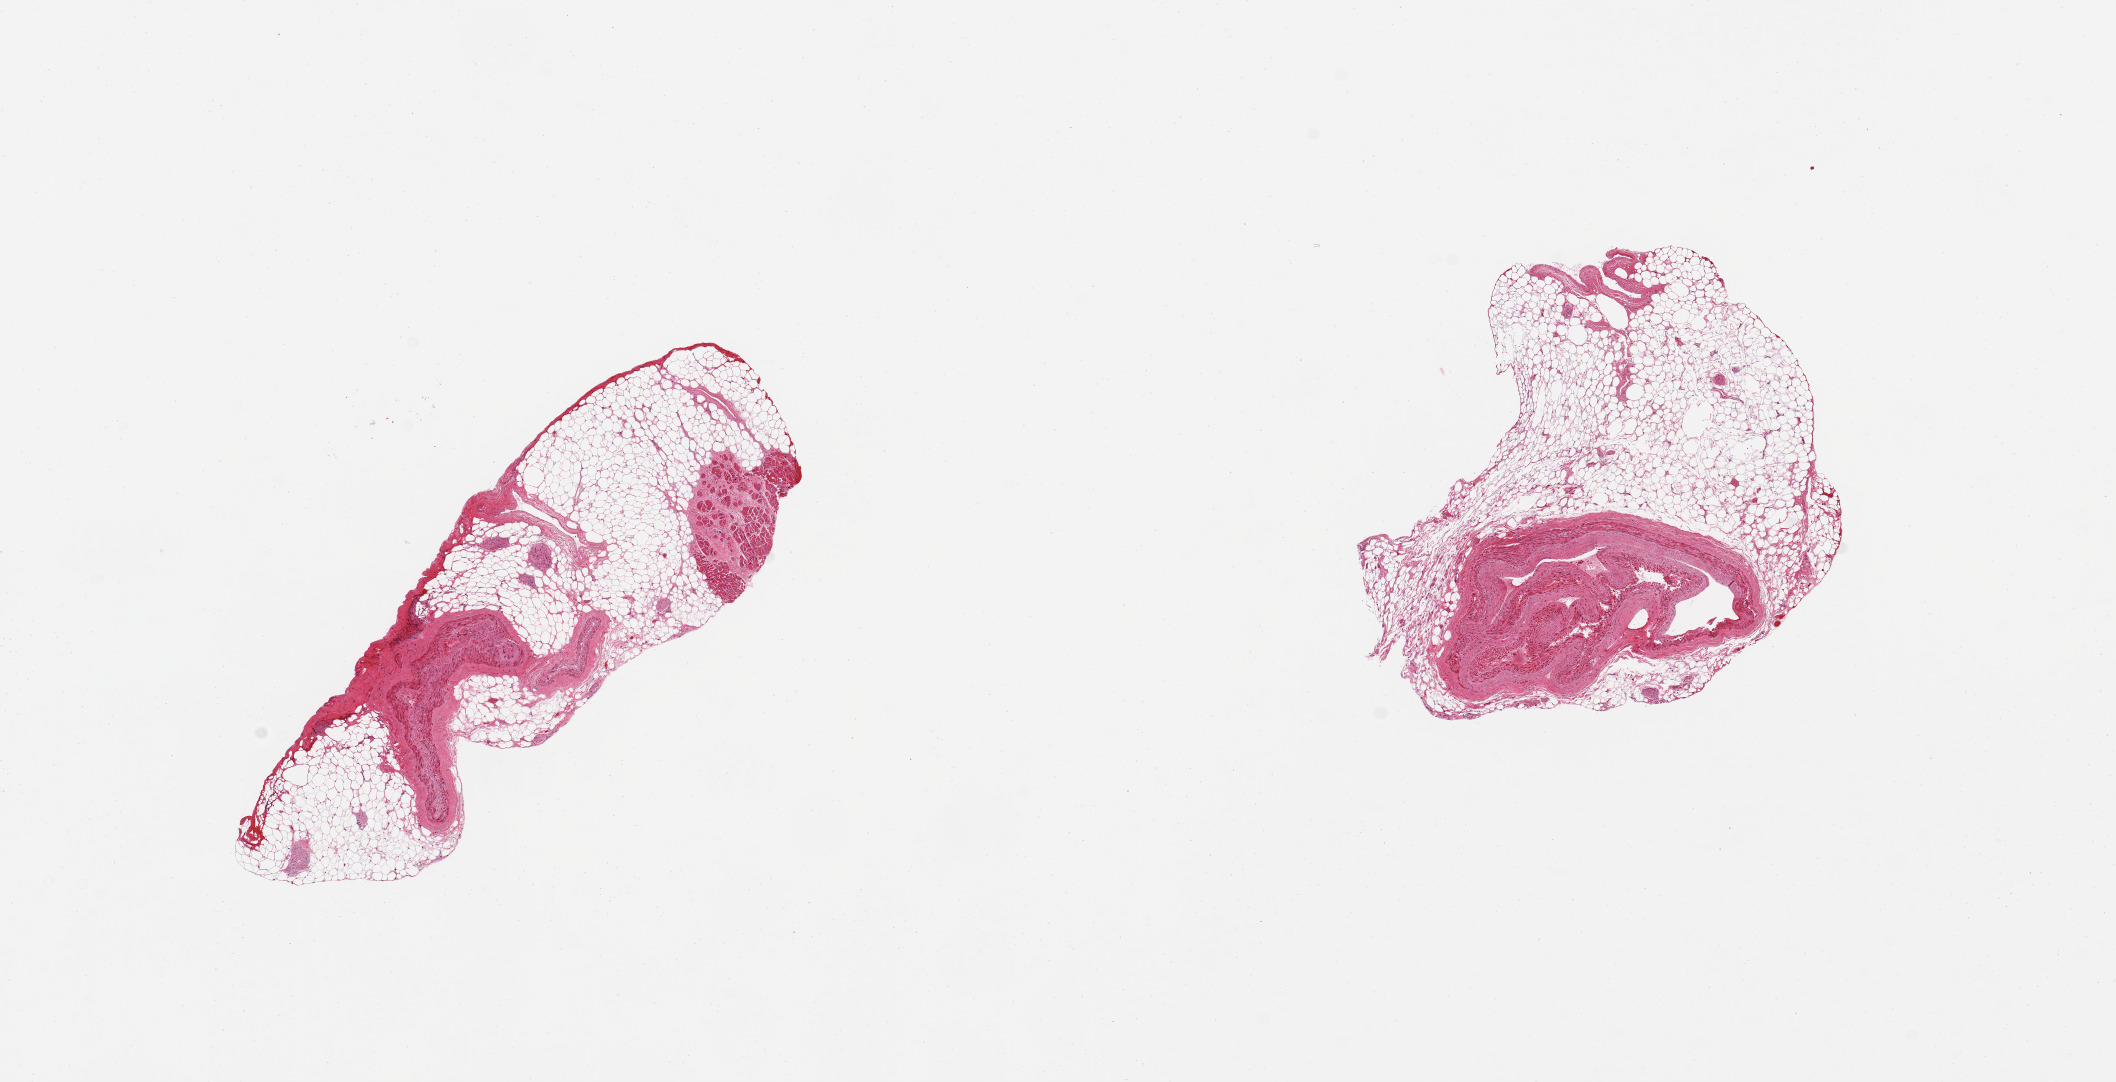
Whole-slide image, haematoxylin and eosin stain, low-resolution overview of the scanned area, about 16.7 x 8.6 mm (slide scanned at 20x); PAXgene-fixed paraffin-embedded (PFPE) section; target tissue: coronary artery; donor tissue sample. Donor sex: male.
Reviewer comment on this tissue sample: 2 pieces; mostly adipose tissue/nerve/and fragment of myocardium with scarring, smaller proportion of artery.